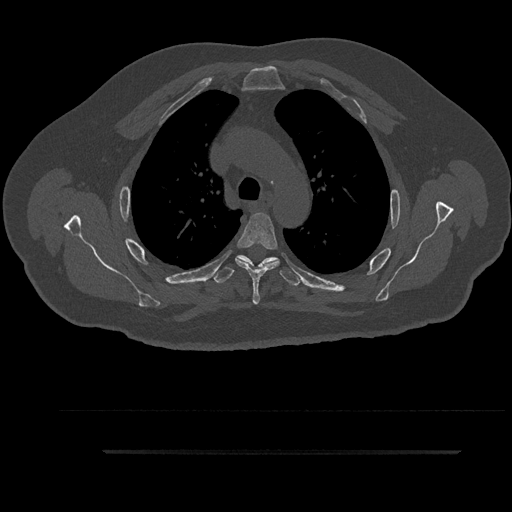
CT including the spine, one axial slice; position 660 of 797 along the scan axis; reconstruction kernel Br40s/3; bone window (W 1800 / L 400 HU); 0.5 mm slice thickness; 512 × 512 image matrix. Male patient, age 63 years. From the clinical record (not read from this slice): primary cancer: renal; vertebrae with lytic lesions (as recorded): T8.
Structures marked on this image (semi-automatically segmented with operator editing):
- T3 vertebra: bounding box [x1, y1, x2, y2] px = [221, 276, 300, 283]
- T4 vertebra: [235, 213, 280, 305]
- T5 vertebra: [213, 255, 300, 286]